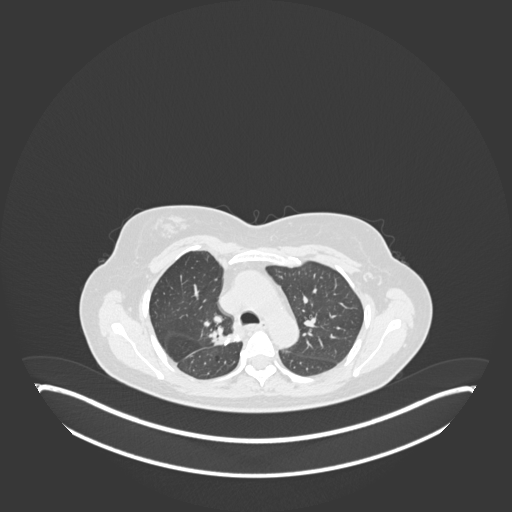
Chest CT, one axial slice; position 120 of 181 along the scan axis; reconstruction kernel B30f; 120 kVp; lung window (W 1500 / L -600 HU); 1 mm slice thickness; 512 × 512 image matrix, field of view 500 × 500 mm. Patient: female, 65 years. From the clinical record (not read from this slice): clinical TNM (as recorded): T1b N0 M0; histopathological grade: G2.
Structures marked on this image (rectangle marked by the reading radiologist):
- lung tumour (recorded histology: adenocarcinoma): bounding box (x1, y1, x2, y2) in pixels: (209, 323, 238, 349)